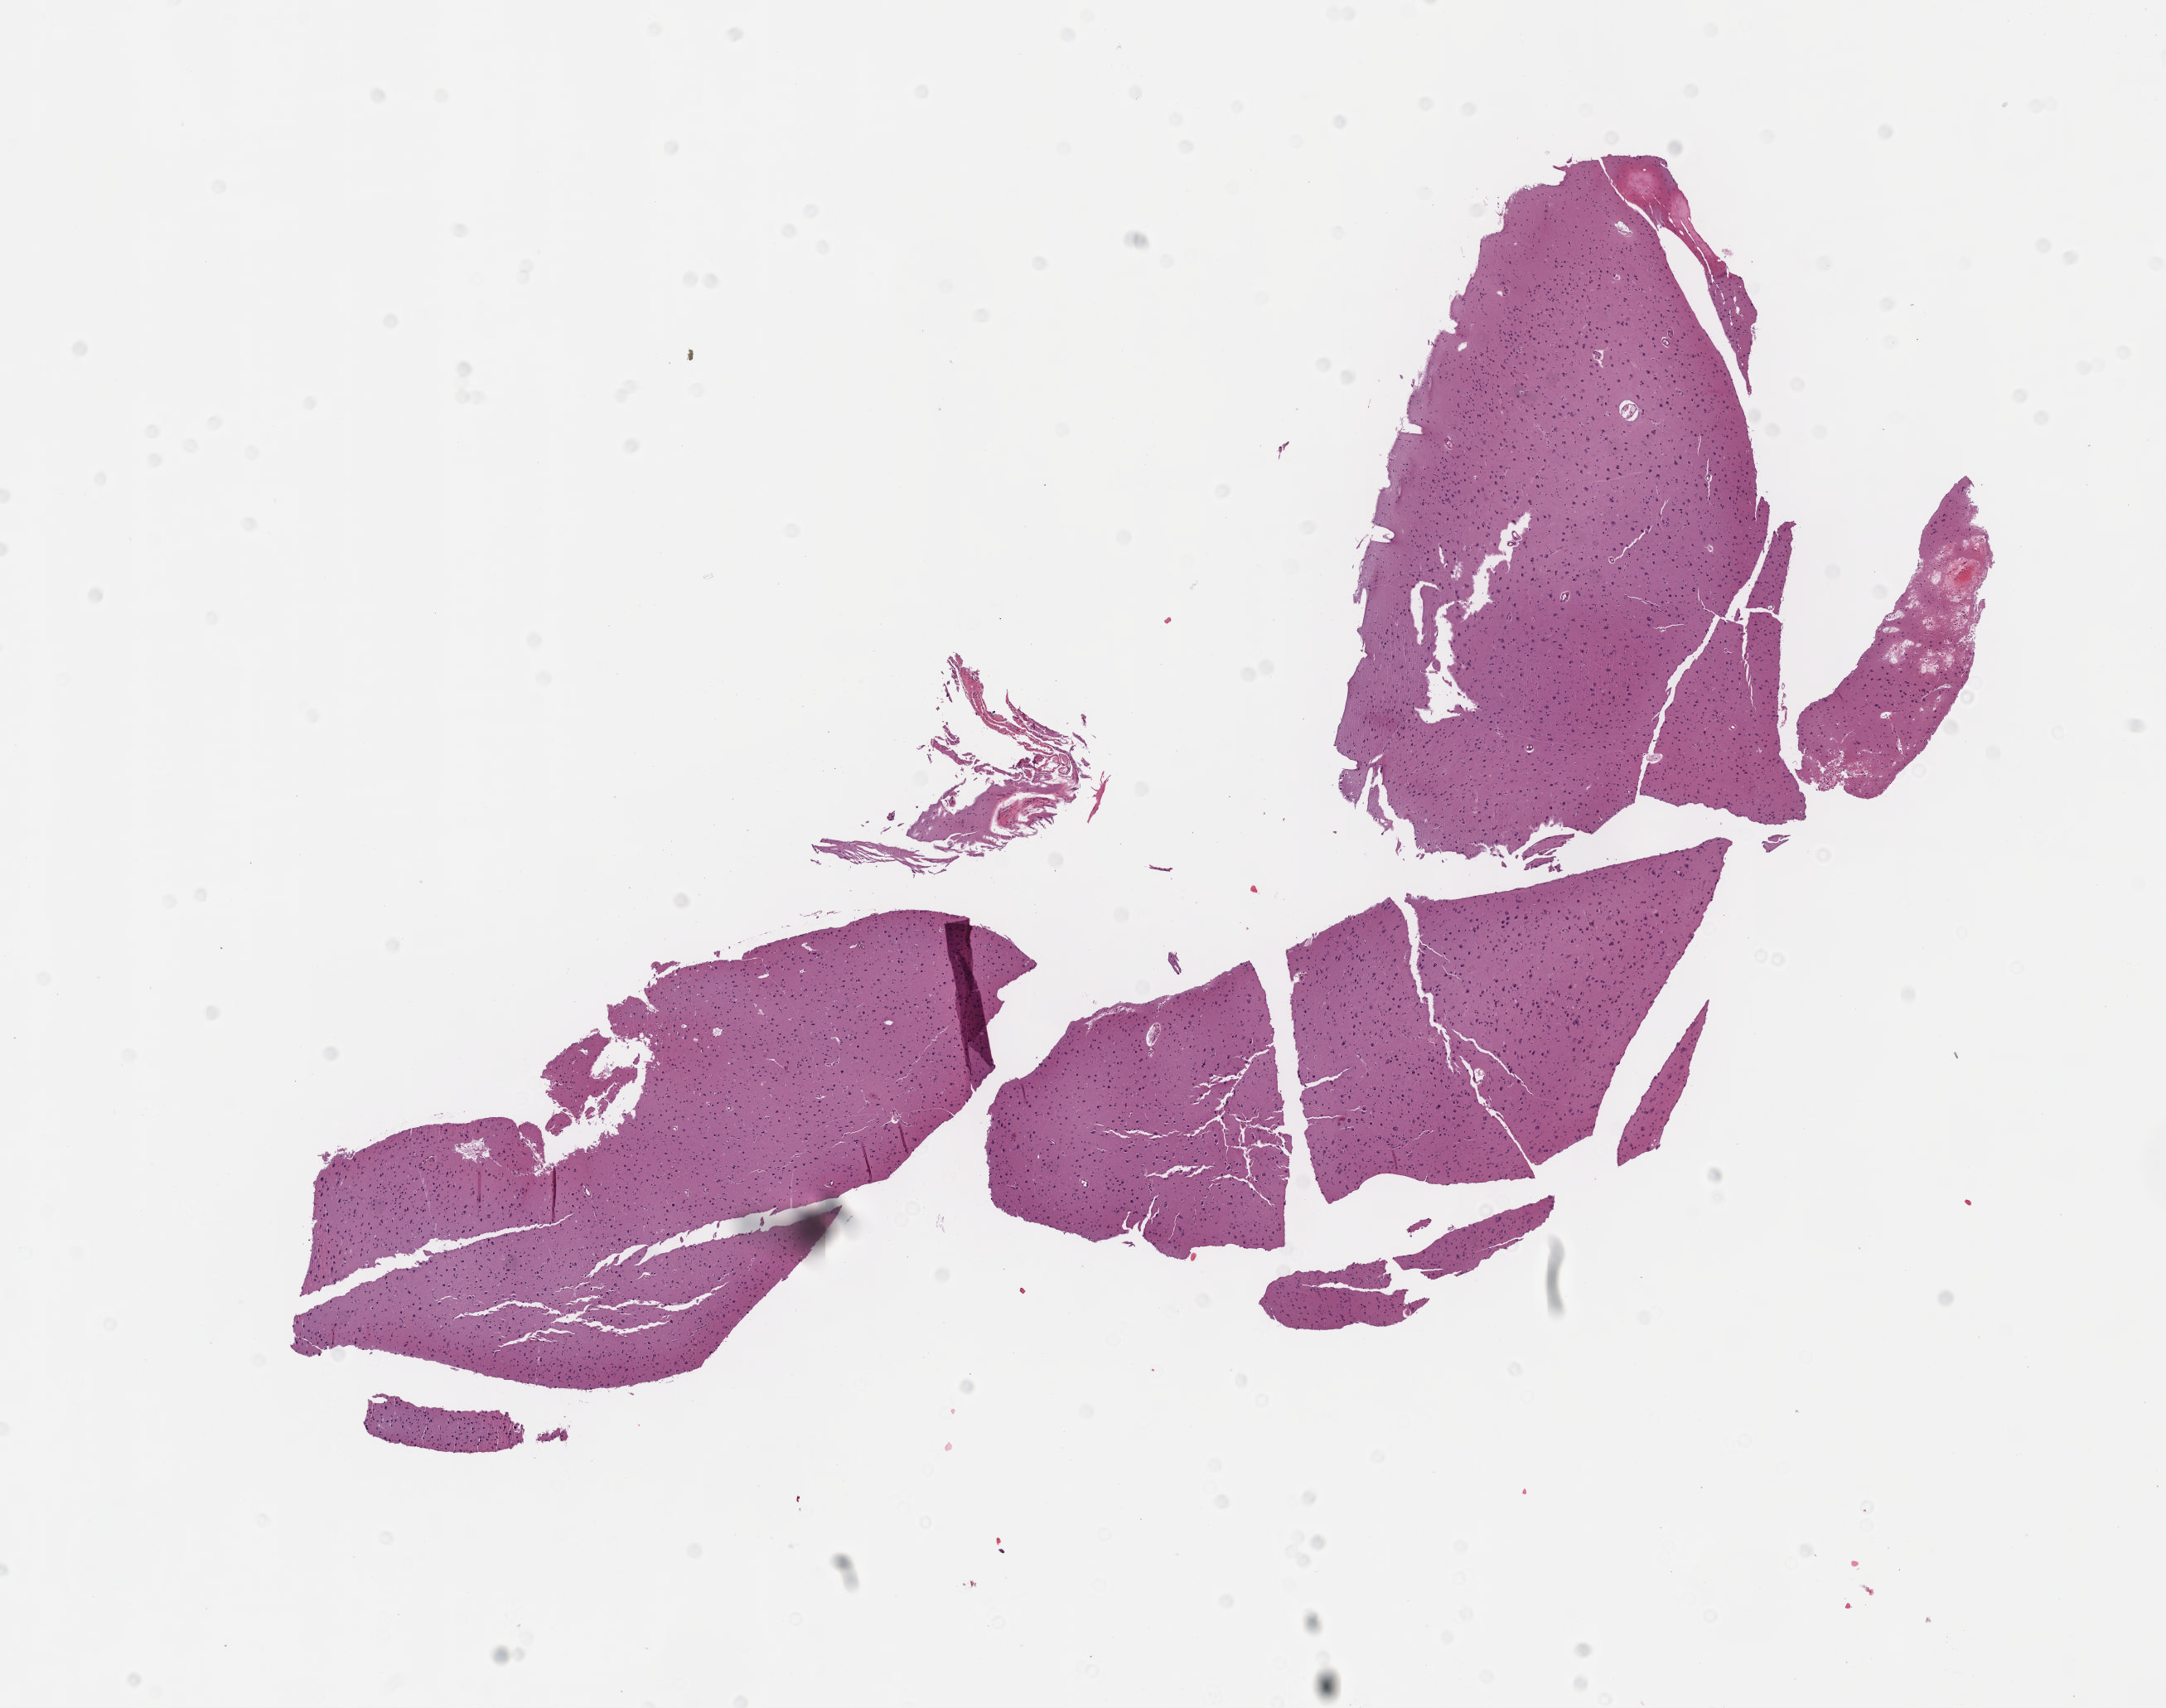
Digitized H&E-stained tissue section (whole slide) — a low-resolution overview of the entire scanned area, about 10.6 x 8.3 mm; FFPE section; brain, primary tumour sample. Female, age 18 years at initial diagnosis. Histologic grade: G2 (moderately differentiated).
Diagnosis: Mixed glioma.